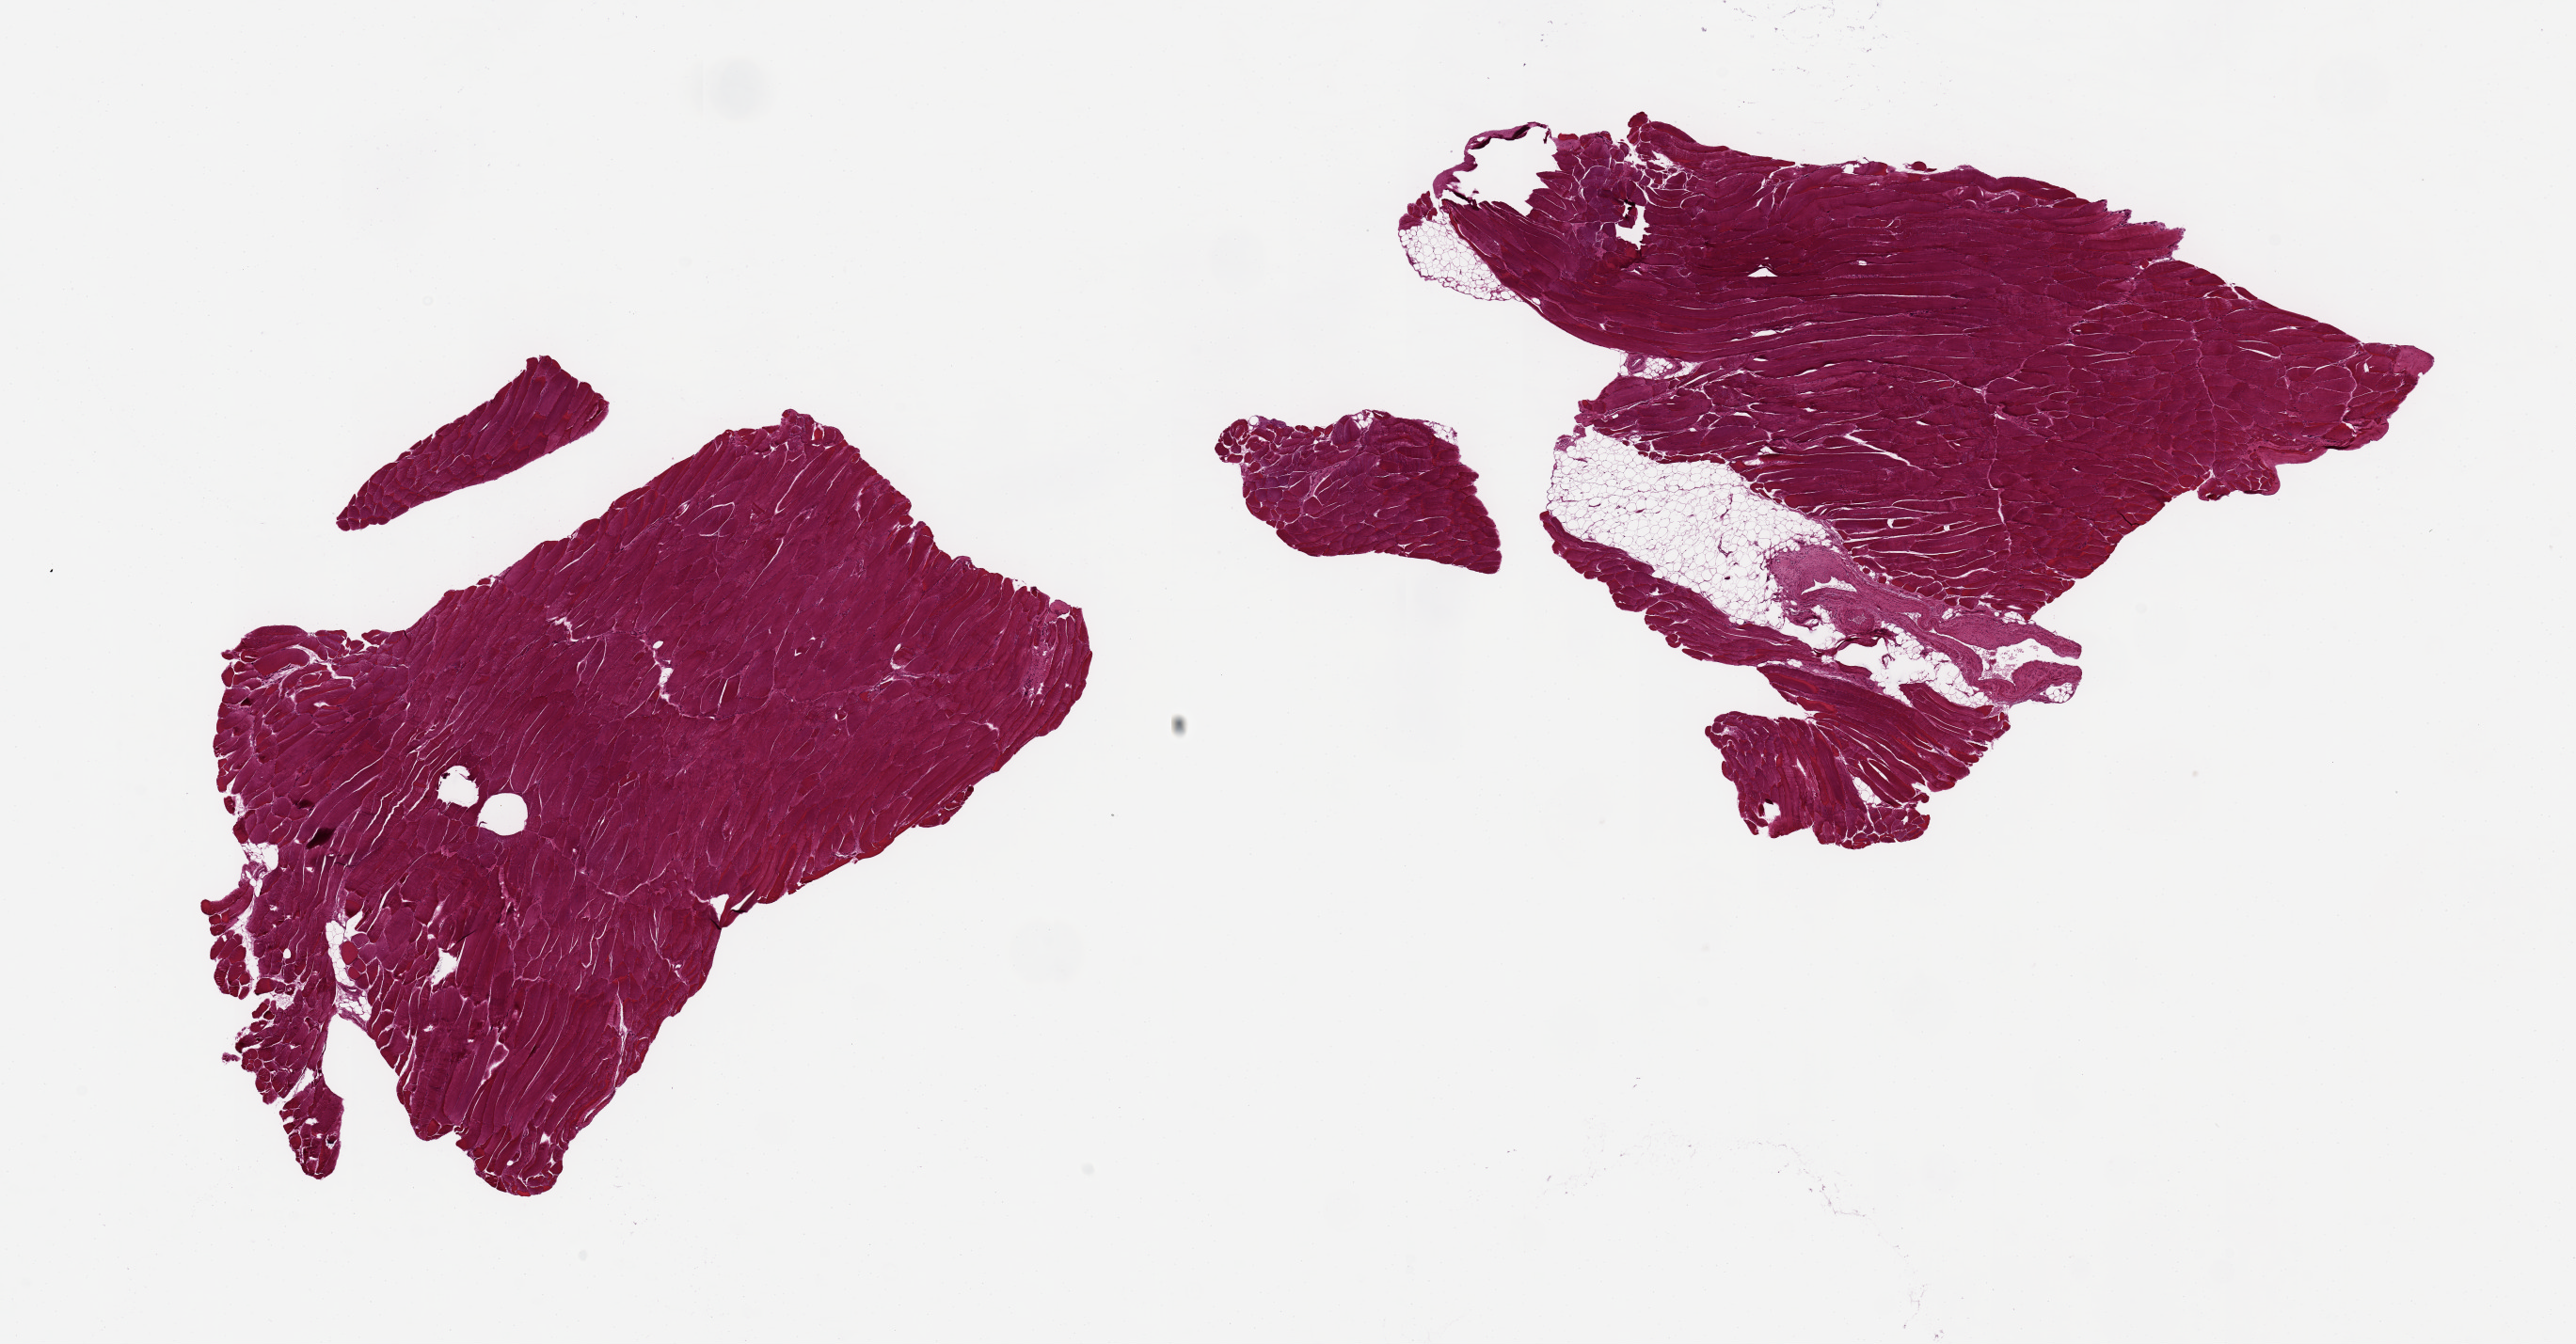
Whole-slide image, haematoxylin and eosin stain, low-resolution overview of the scanned area, about 21.7 x 11.3 mm. PAXgene-fixed, paraffin-embedded tissue. Target tissue: skeletal muscle. Donor tissue sample. Donor sex: male.
Pathologist's review note for this sample: 2 aliquots, 6x5mm. ~10% interstitial fat, one aliquot.